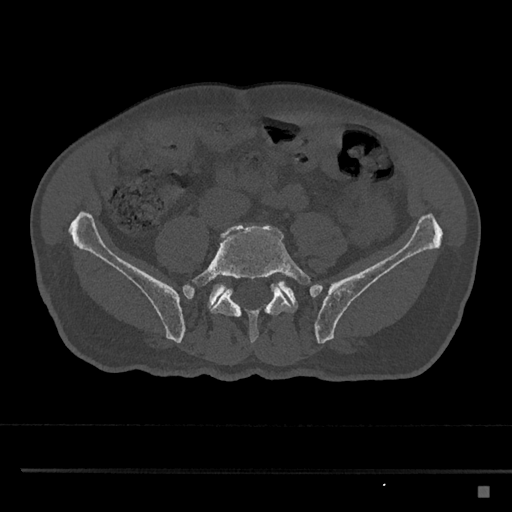
CT including the spine, one axial slice. Position 574 of 797 along the scan axis. Reconstruction kernel Br40s/3. Bone window (W 1800 / L 400 HU). 0.5 mm slice thickness. 512 × 512 image matrix. Patient: male, 59 years. From the clinical record (not read from this slice): primary cancer: prostate.
Structures marked on this image (semi-automatically segmented with operator editing):
- L5 vertebra: bounding box (x1, y1, x2, y2) in pixels: (183, 224, 312, 343)